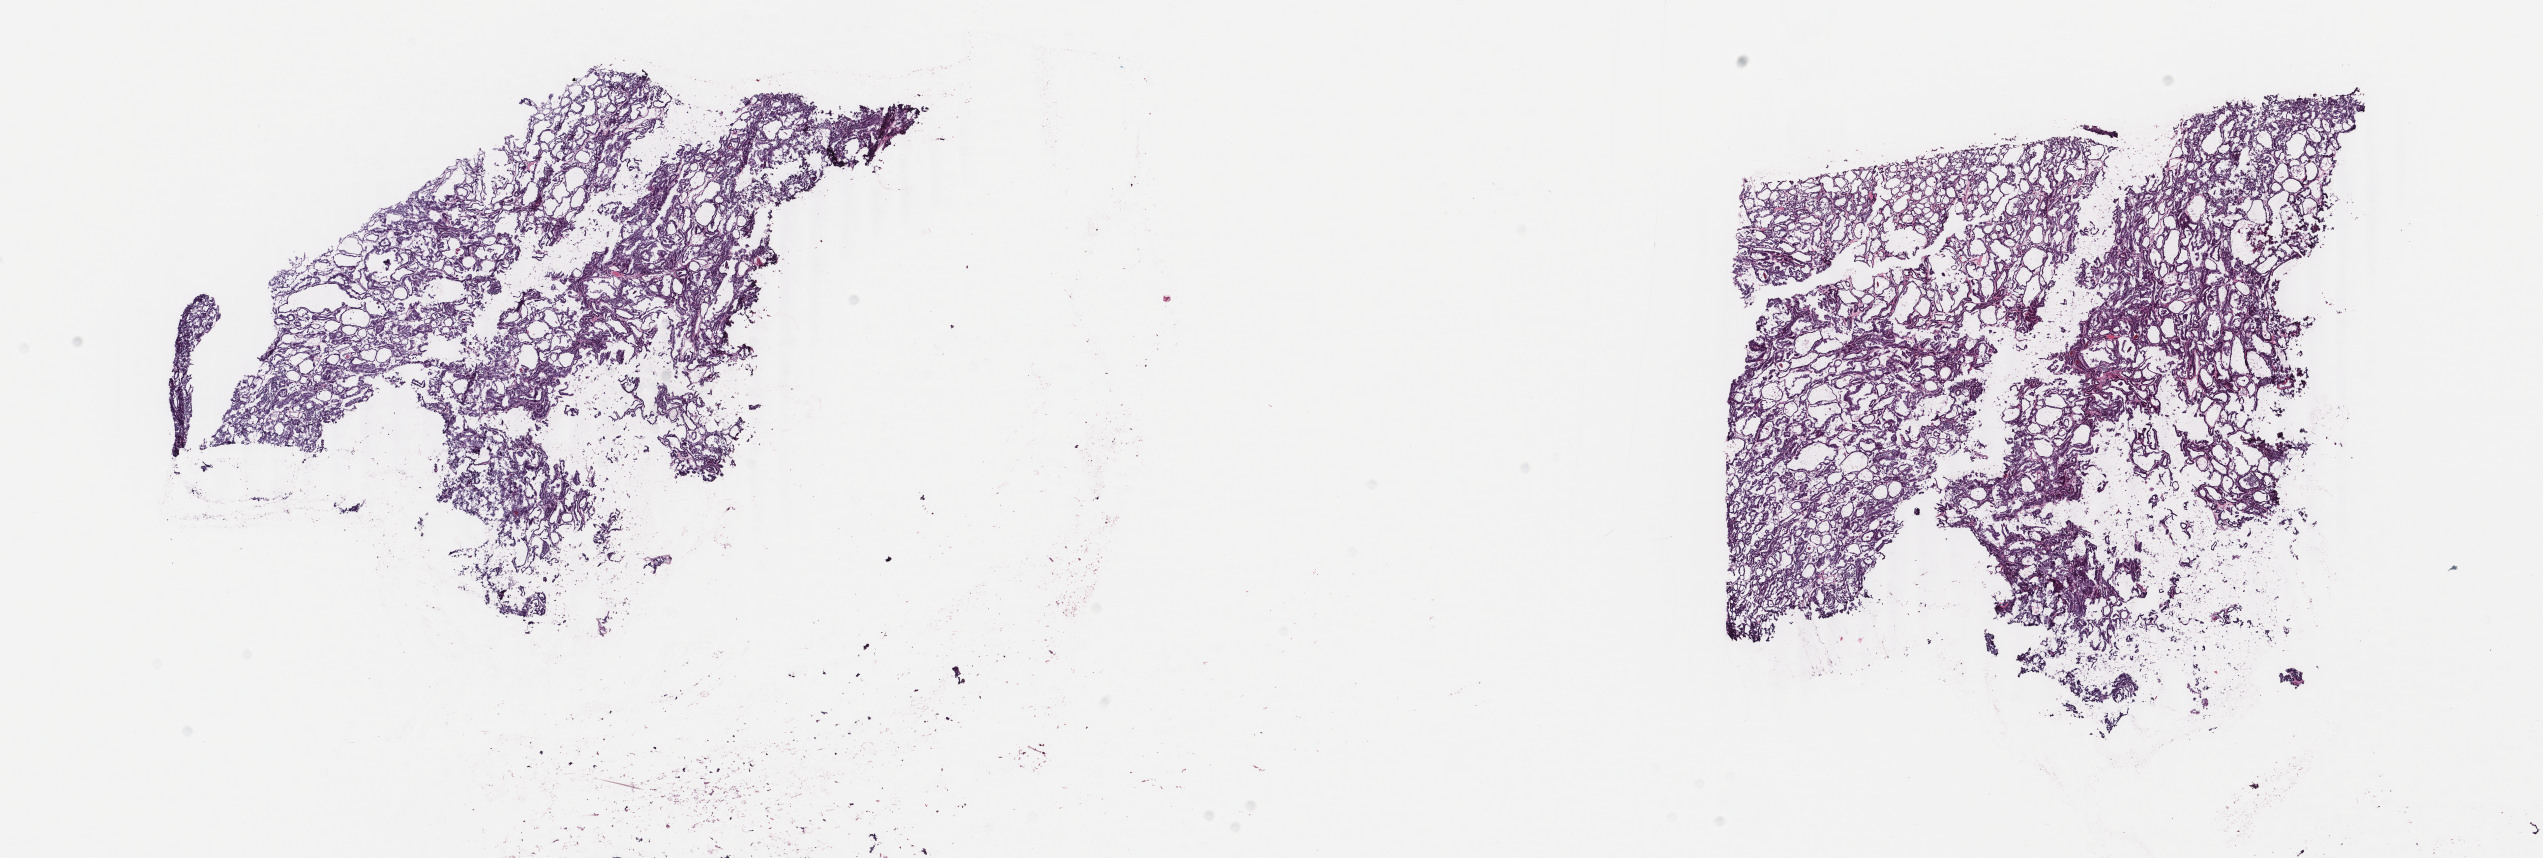
Whole-slide histology image, Hematoxylin and eosin (H&E) stained, whole scanned area (about 20.2 x 6.8 mm) shown as a low-resolution overview. Frozen section from the bottom of the tissue portion. Sample: primary tumour, thyroid. Male patient; age at initial diagnosis 50 years. Slide review estimates, as recorded: tumour cells 100%, tumour nuclei 95%, normal cells 0%, stromal cells 0%, necrosis 0%. Inflammatory infiltration, as recorded: lymphocyte infiltration 0%, monocyte infiltration 0%, neutrophil infiltration 0%.
AJCC pathologic stage: III (7th edition). Laterality: right. Histologic diagnosis: Papillary carcinoma, follicular variant (thyroid gland). Lymph nodes positive (case pathology): 0 of 2 examined.